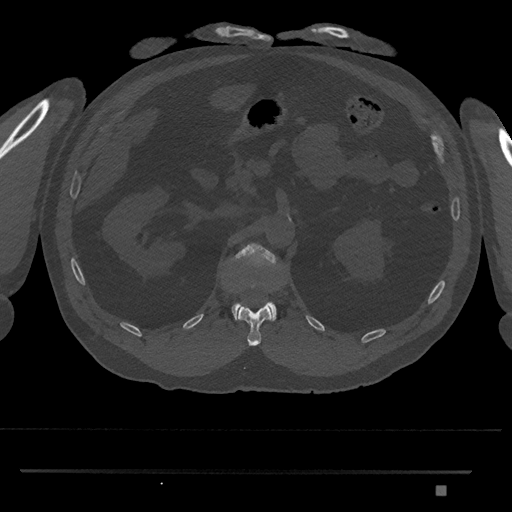
CT including the spine, one axial slice; position 860 of 1134 along the scan axis; 120 kVp; bone window (W 1800 / L 400 HU); 0.5 mm slice thickness; 512 × 512 image matrix, field of view 429 × 429 mm. Patient: male, 65 years. Case-level facts recorded for this patient, not image findings: primary cancer: prostate.
Outlined on this slice (semi-automatic segmentation, software-assisted and operator-edited):
- L1 vertebra: bounding box [x1, y1, x2, y2] px = [231, 243, 278, 321]
- T12 vertebra: [237, 304, 272, 346]